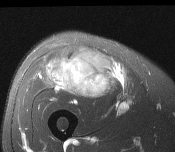
MRI of an extremity soft-tissue mass, one axial slice. Position 76 of 116 along the scan axis. T2-weighted fat-saturated. MR volume resampled by the dataset authors to the PET/CT grid (not the native acquisition matrix). 3.27 mm slice thickness. 175 × 152 image matrix, field of view 171 × 148 mm. Male patient. From the clinical record (not read from this slice): histological type: pleiomorphic leiomyosarcoma; grade: intermediate; site of the primary tumour: right thigh.
Outlined on this slice (expert contour drawn on MRI and transferred to this co-registered scan by the dataset authors):
- gross tumour volume including surrounding oedema: bounding box (x1, y1, x2, y2) in pixels: (47, 49, 114, 98)
- gross tumour volume (mass): (47, 49, 114, 98)